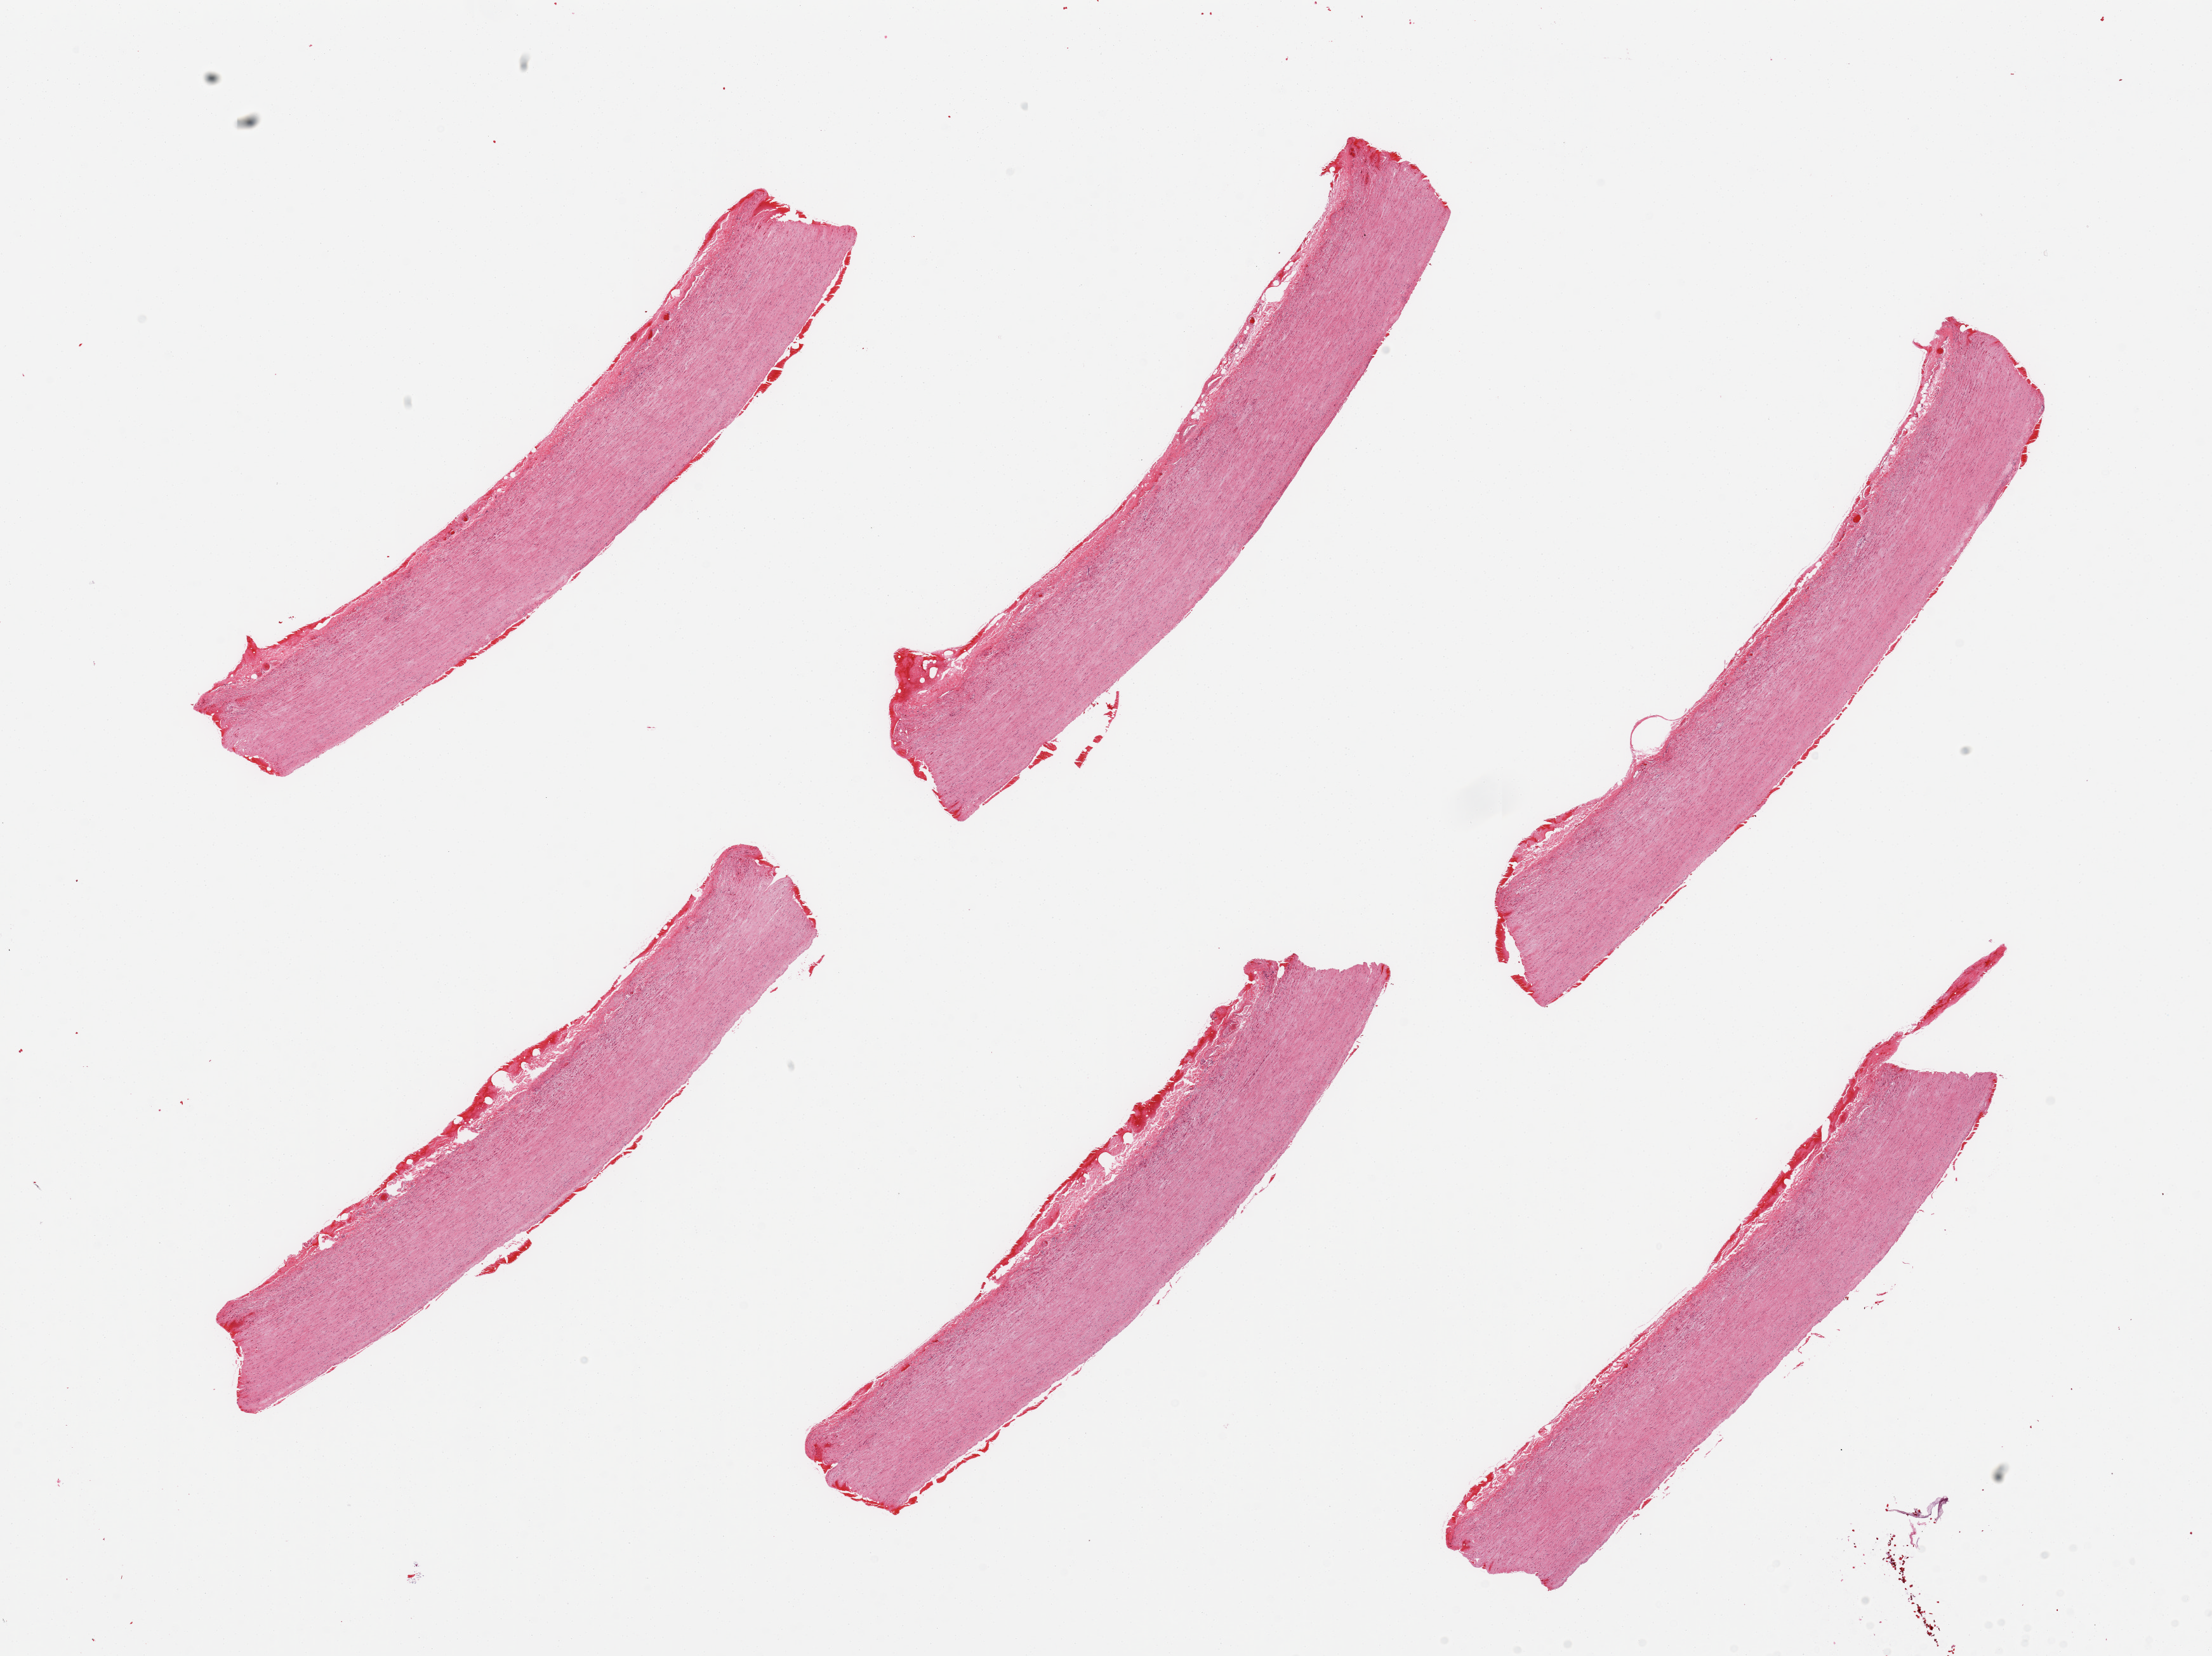
Hematoxylin and eosin (H&E) whole-slide image, low-resolution overview of the scanned area, about 27.6 x 20.6 mm (from a 20x scan). PAXgene-fixed, paraffin-embedded tissue. Target tissue: aorta. Tissue donor sample. Male donor.
* pathologist's review note for this sample: 6 pieces, trace adherent serosa, ~0.3mm thick, on a few sections